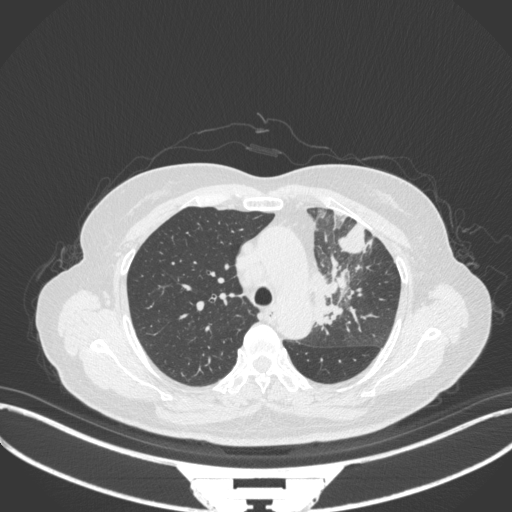
Chest CT, one axial slice. Slice 241 of 382 in the series (ordered by position). 120 kVp. Lung window (W 1500 / L -600 HU). 1 mm slice thickness. 512 × 512 image matrix, field of view 400 × 400 mm. Female patient, age 64 years. Case-level facts recorded for this patient, not image findings: clinical TNM (as recorded): T2a N2 M0.
Outlined on this slice (bounding box drawn by a radiologist):
- lung tumour (recorded histology: adenocarcinoma): bounding box (x1, y1, x2, y2) in pixels: (312, 261, 360, 330)
- lung tumour (recorded histology: adenocarcinoma): (336, 218, 373, 260)